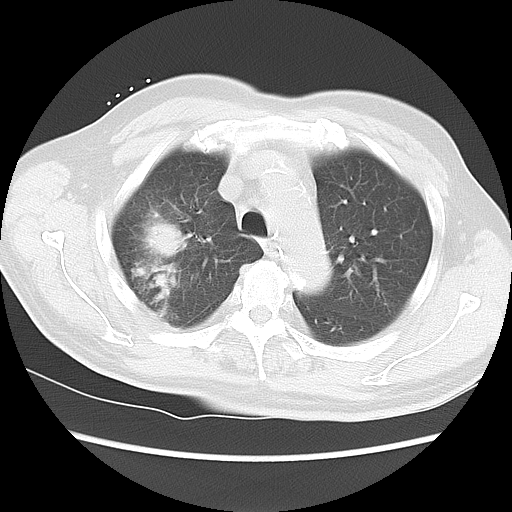
Chest CT, one axial slice; position 15 of 15 along the scan axis; 120 kVp; lung window (W 1500 / L -600 HU); 512 × 512 image matrix, field of view 350 × 350 mm. Patient: male, 68 years. From the clinical record (not read from this slice): clinical TNM (as recorded): T4 N3 M0.
Annotated regions visible in this slice (bounding box drawn by a radiologist):
- lung tumour (recorded histology: squamous cell carcinoma): bounding box <141,216,199,321> (left, top, right, bottom; pixels)